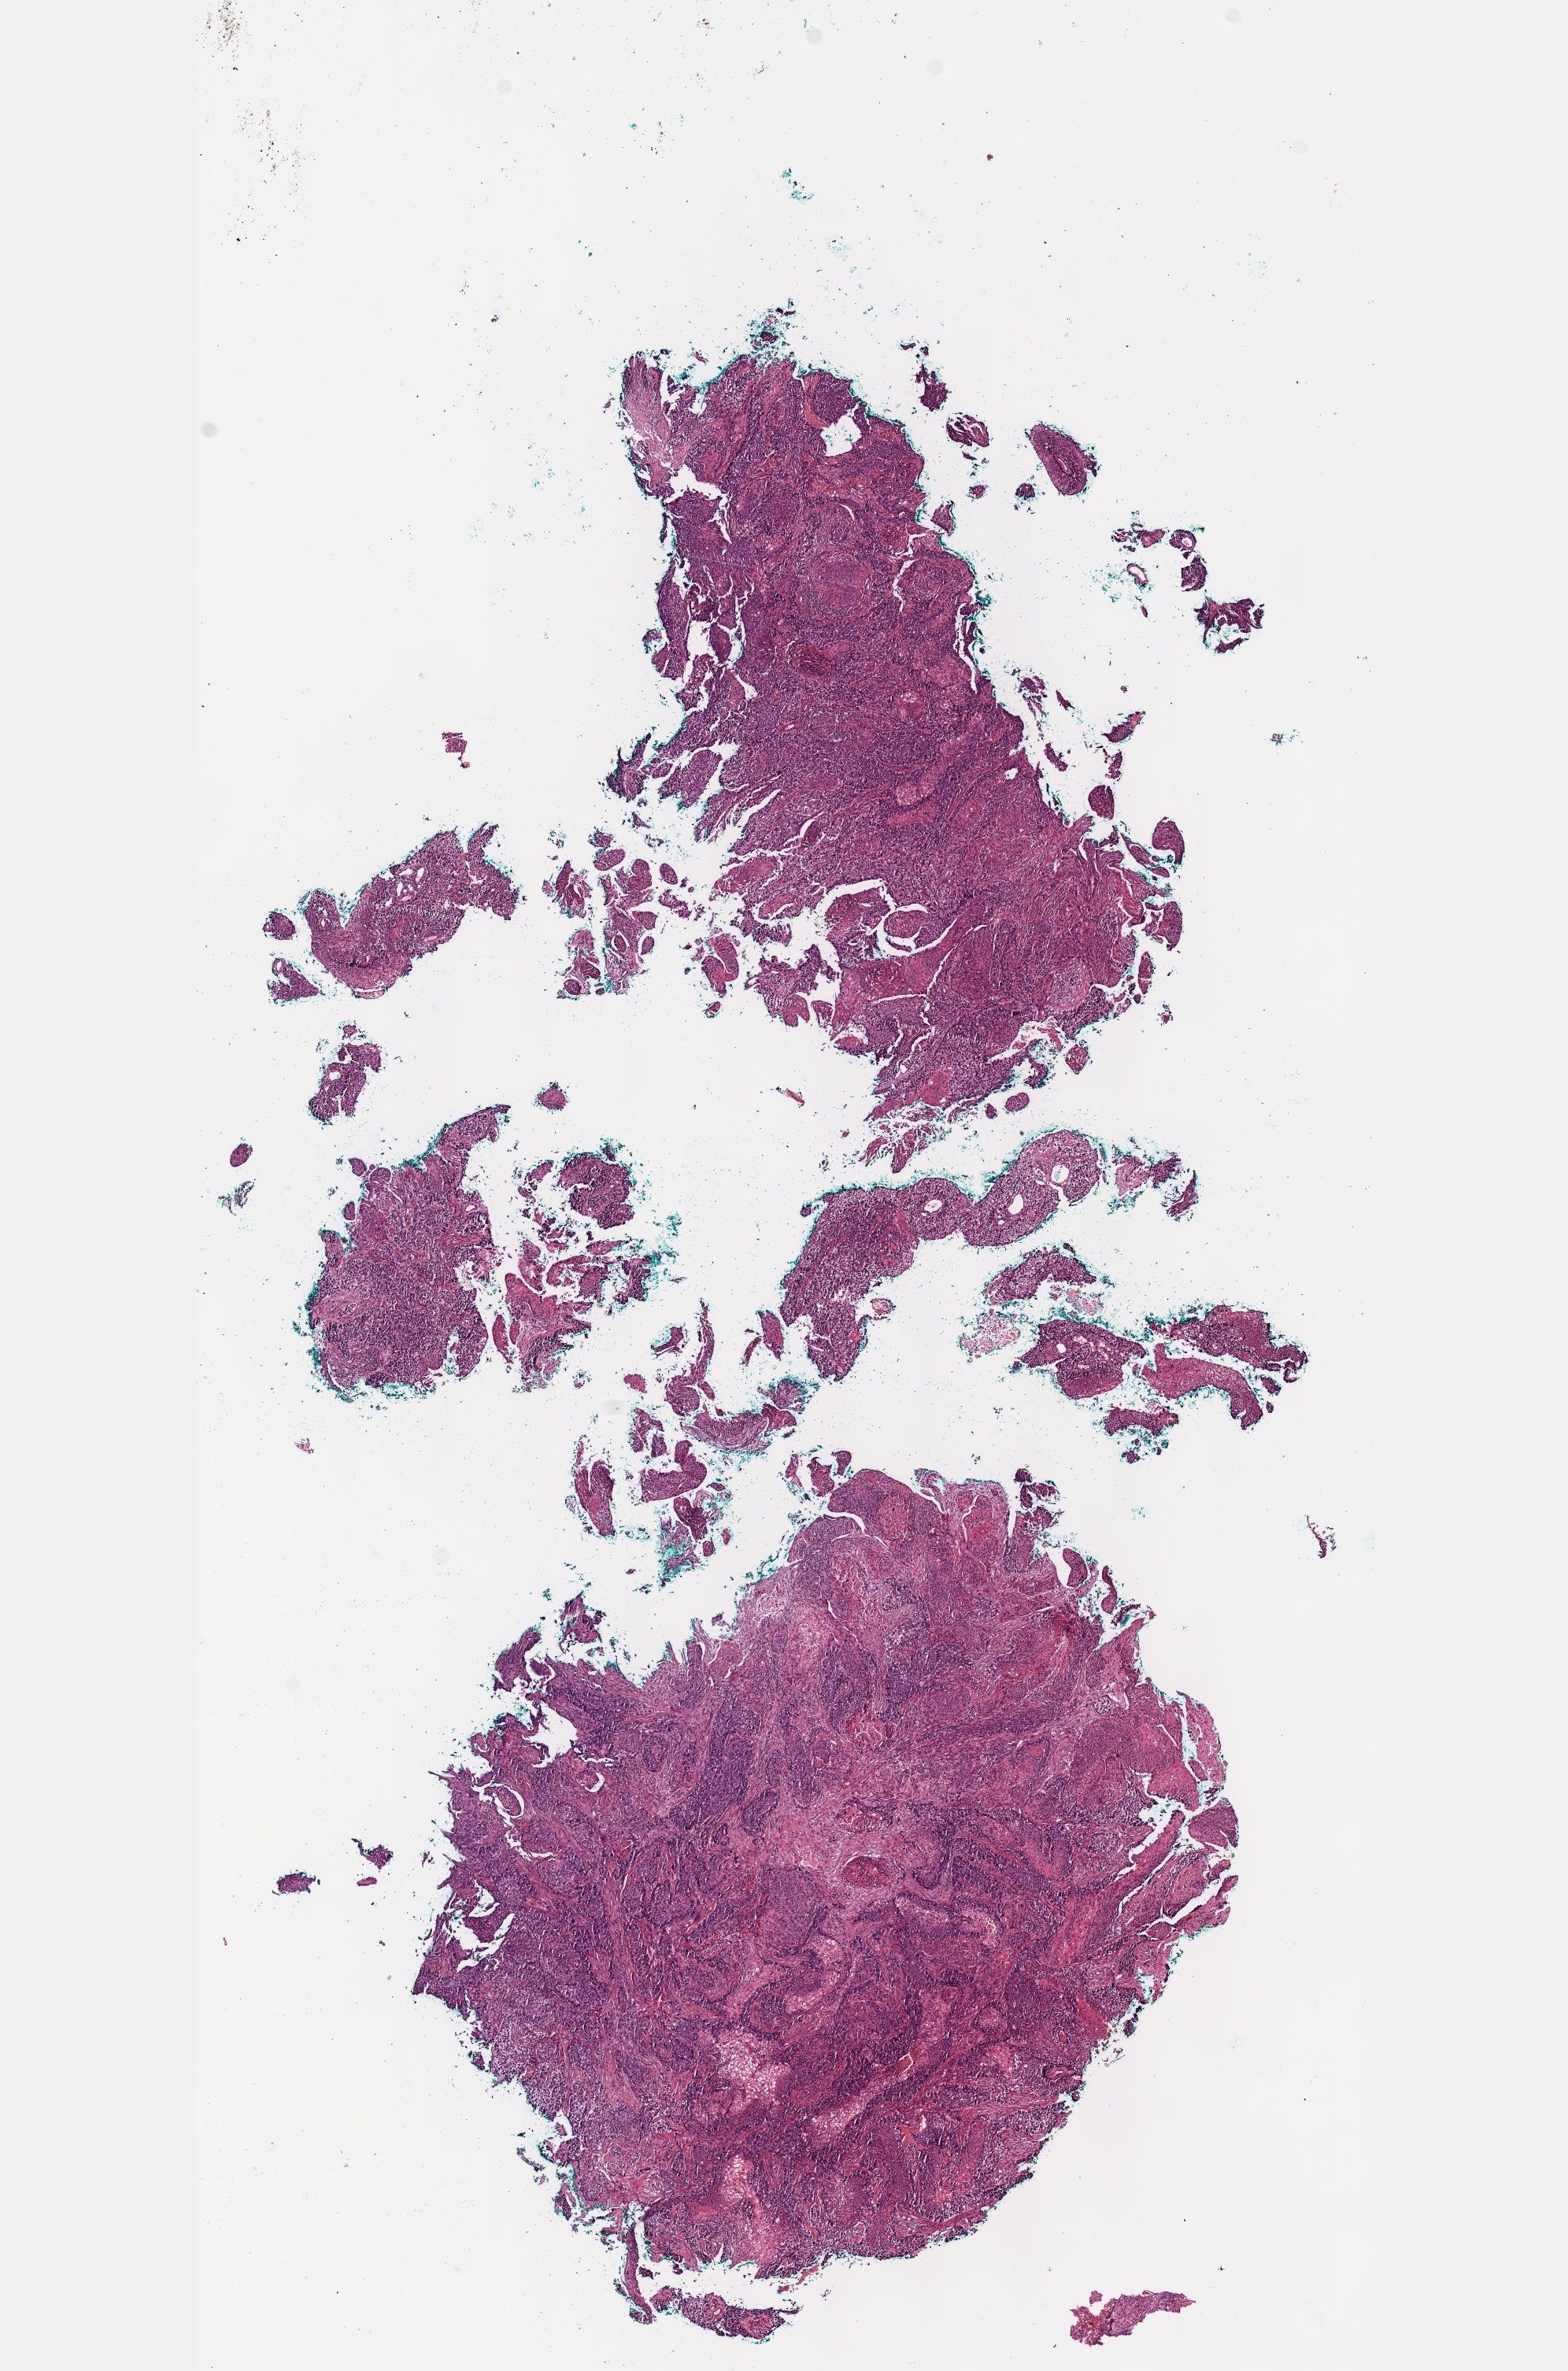
Whole-slide histology image, H&E, whole scanned area (about 8.0 x 12.2 mm) shown as a low-resolution overview. FFPE section. Cervix, primary tumour sample. Female, age 51 years at initial diagnosis. Histologic grade: G2 (moderately differentiated).
FIGO stage: IVA. Diagnosis: Squamous cell carcinoma, NOS (cervix uteri).